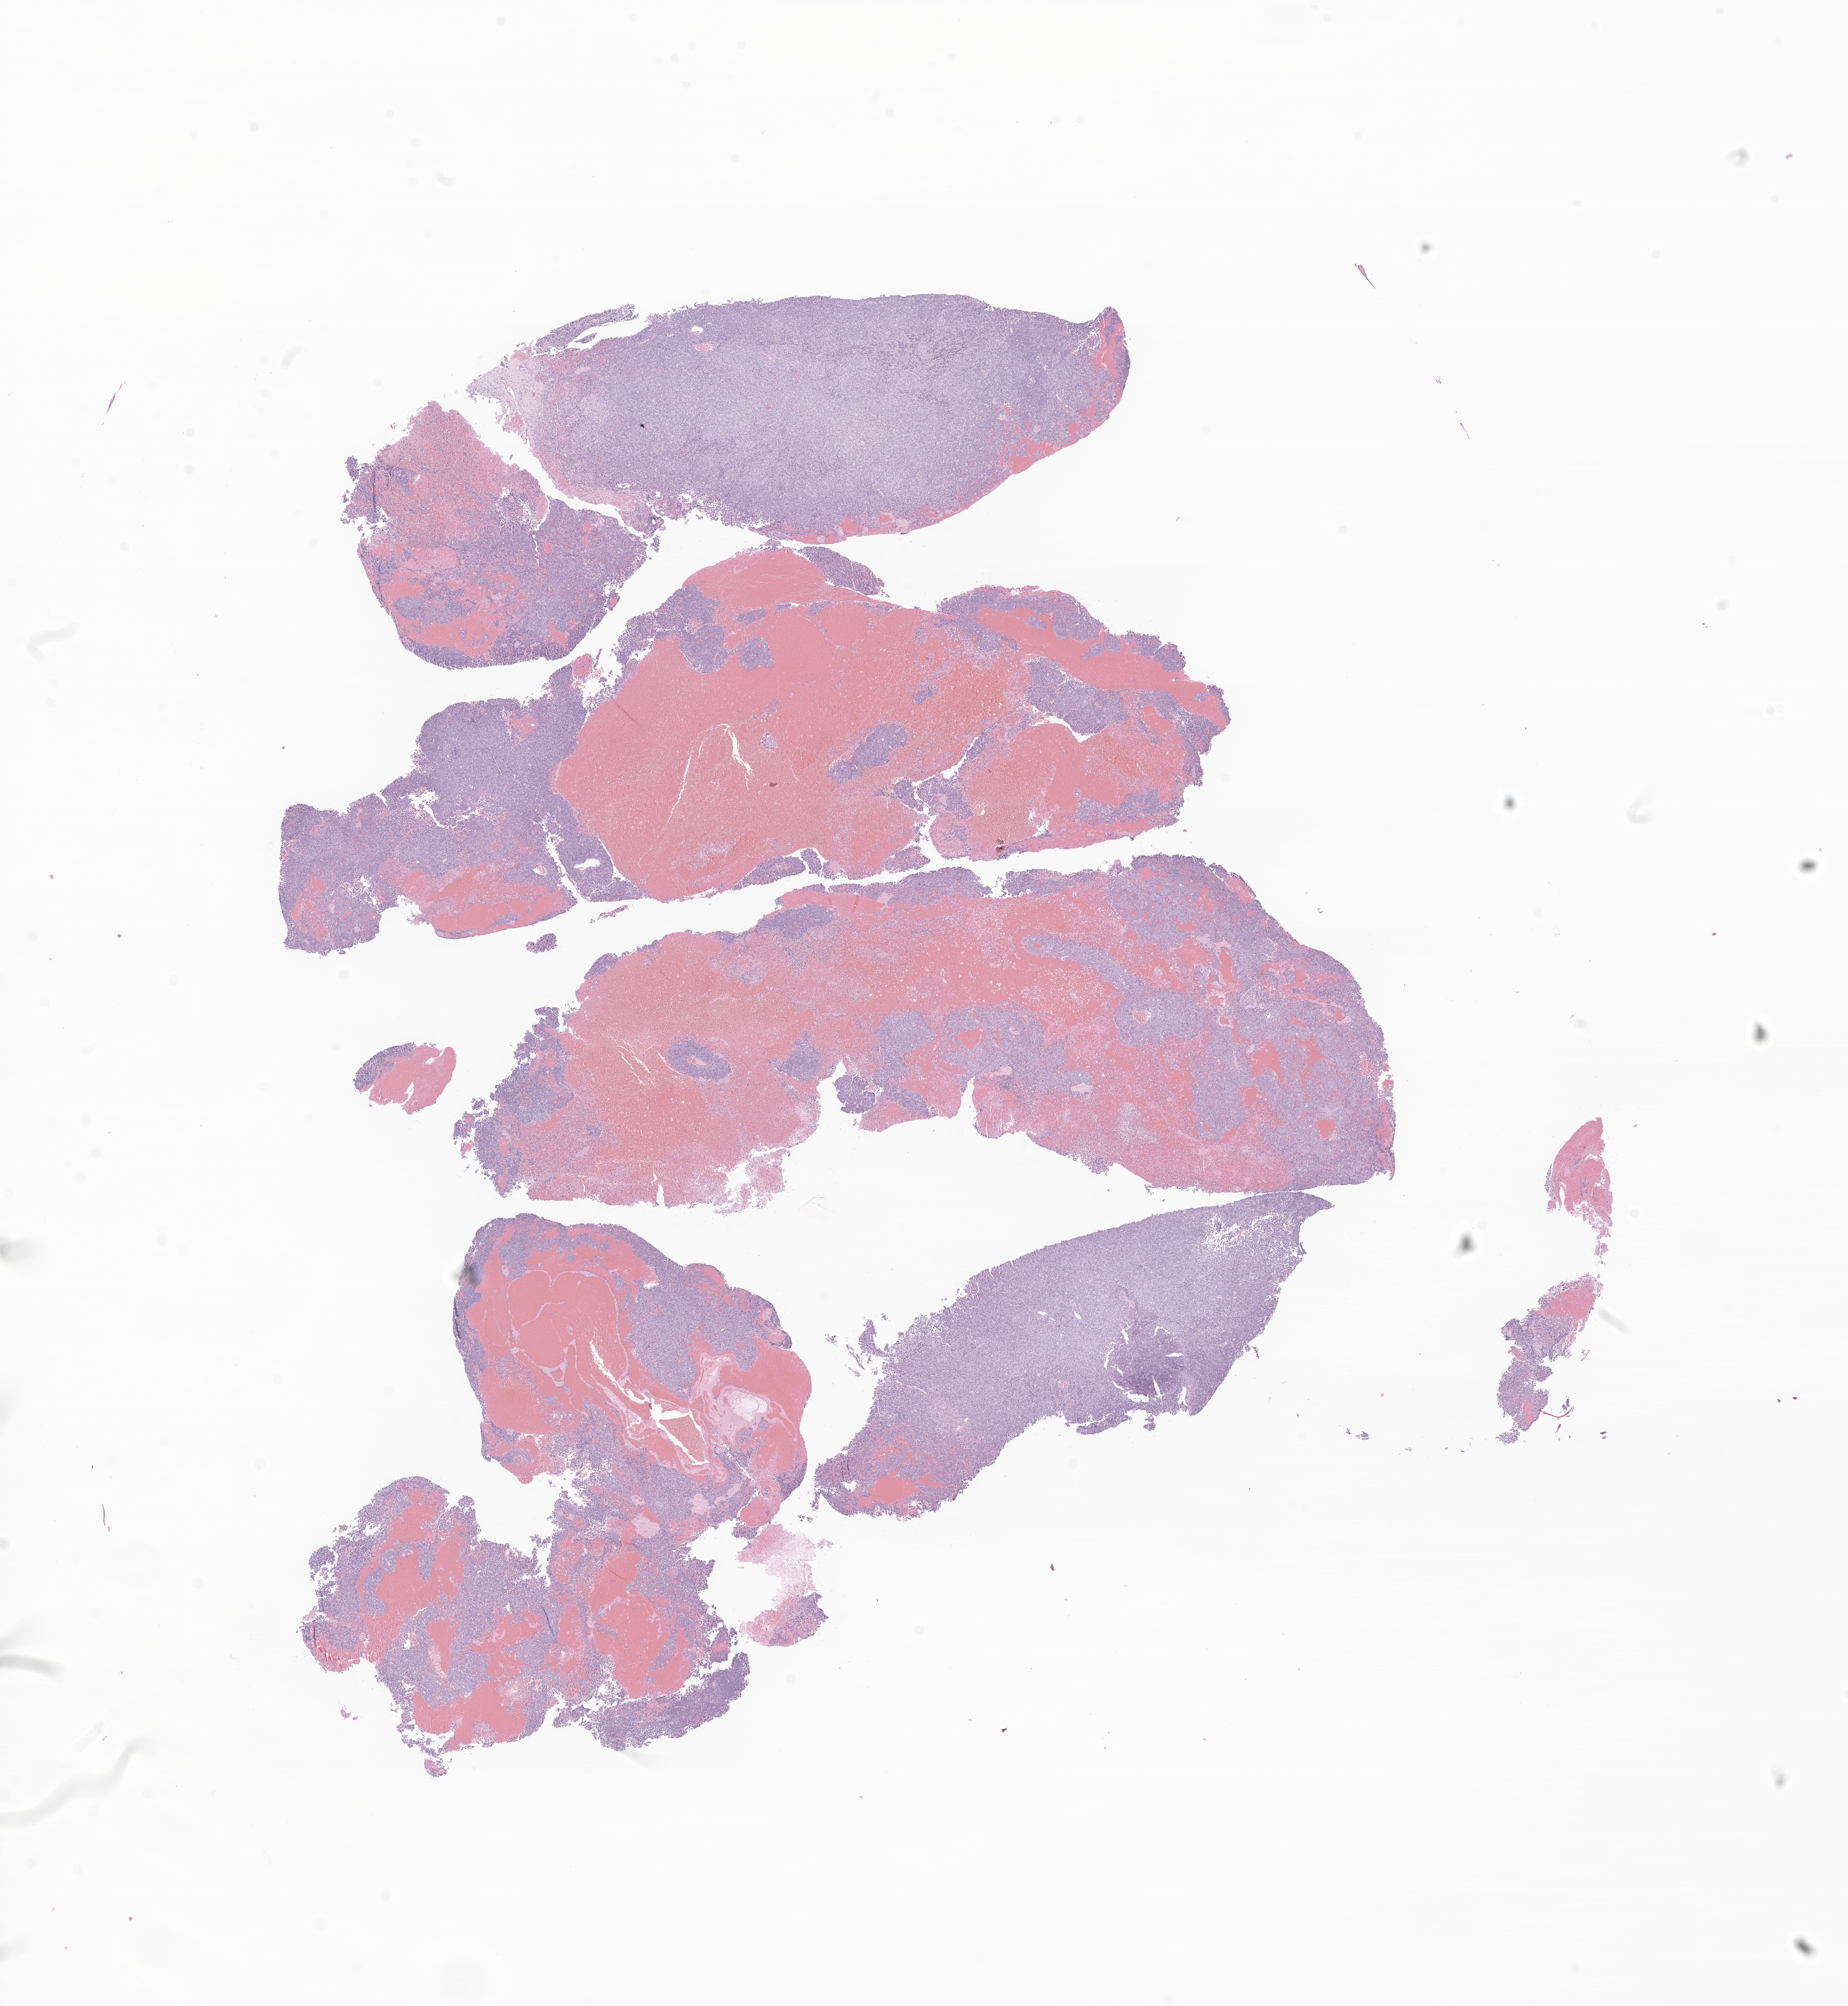
Whole-slide image, hematoxylin and eosin (H&E) stain of tumor tissue from the brain, a low-resolution overview of the entire scanned area, about 16.4 x 17.8 mm; formalin-fixed paraffin-embedded section. Patient male; age 84 days.
- diagnosis (ICD-O-3 morphology term): Neoplasm, malignant